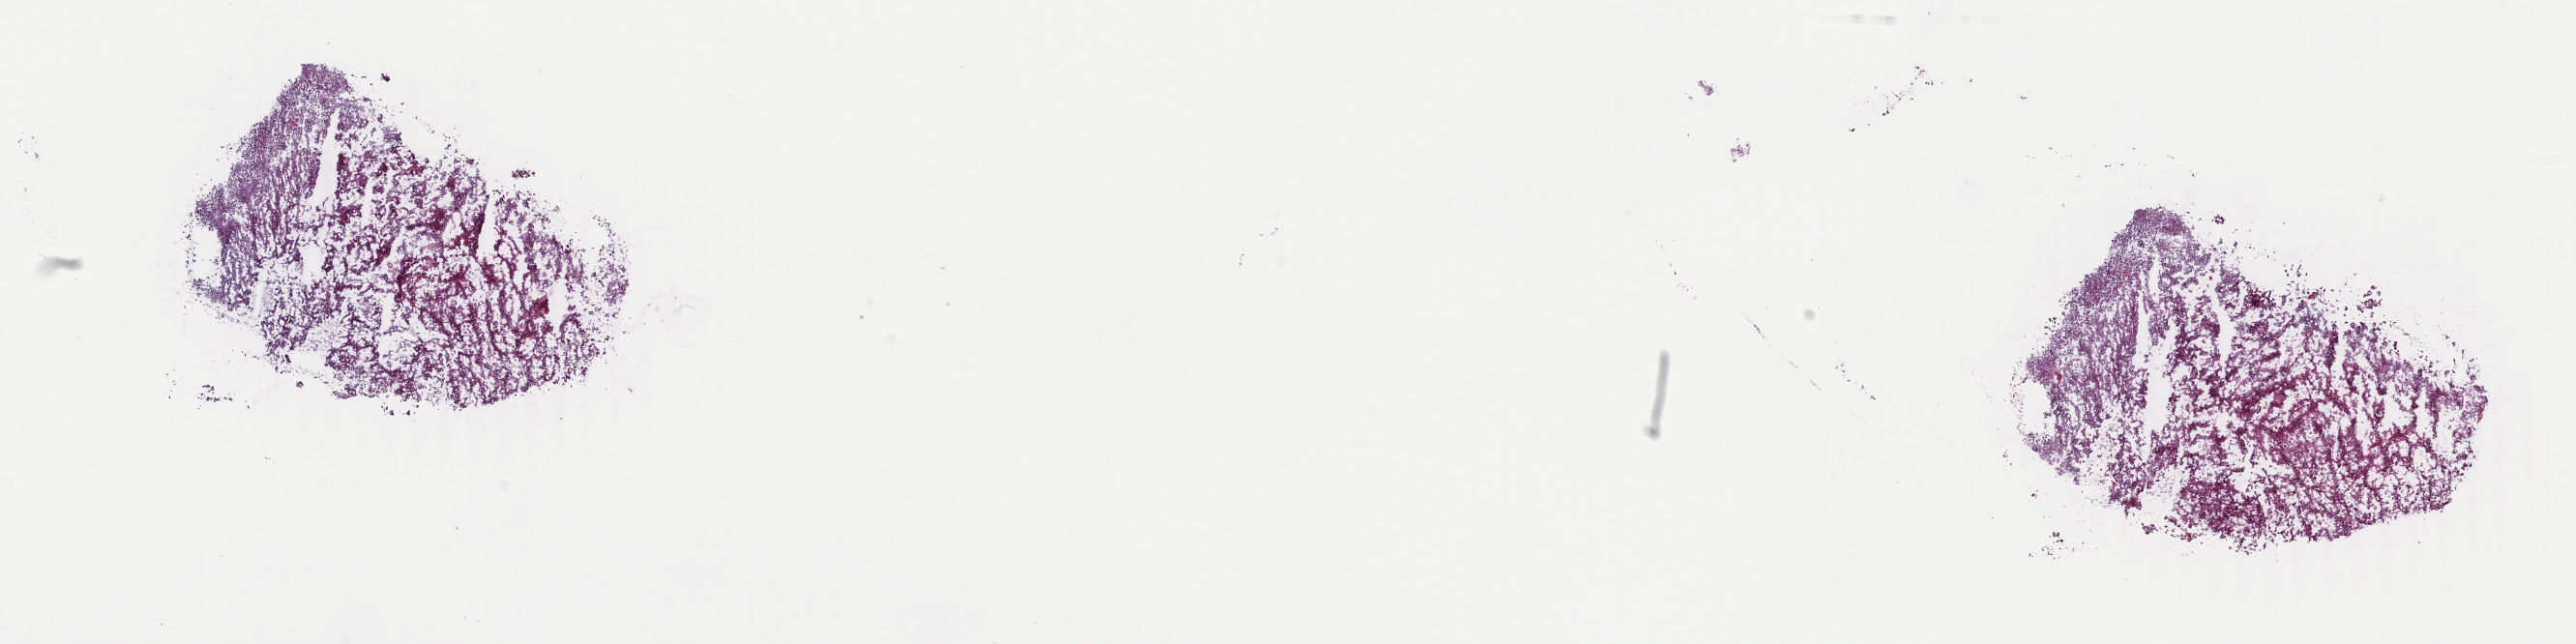
Hematoxylin and eosin (H&E) stained whole-slide image, a low-resolution overview of the entire scanned area, about 21.2 x 5.3 mm. Frozen section from the top of the tissue portion. Brain, primary tumour sample. Female, age 78 years at initial diagnosis. Pathologist review of this section (percent, as recorded): tumour cells 75%, tumour nuclei 80%, normal cells 5%, stromal cells 5%, necrosis 15%. Inflammatory infiltration, as recorded: lymphocyte infiltration 0%, monocyte infiltration 0%, neutrophil infiltration 0%.
* histologic diagnosis: Glioblastoma (occipital lobe)